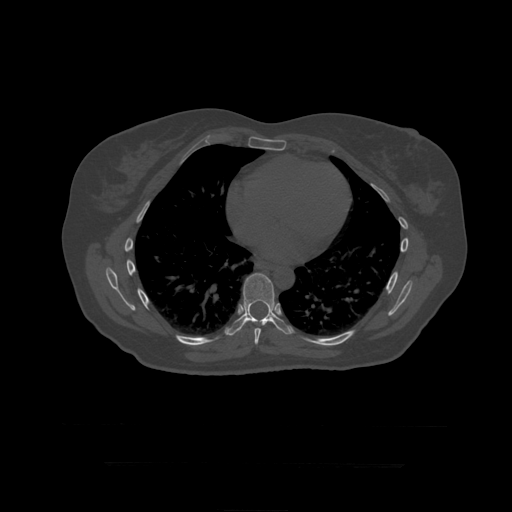
CT including the spine, one axial slice. Slice 268 of 399 in the series (ordered by position). Bone window (W 1800 / L 400 HU). 512 × 512 image matrix, field of view 450 × 450 mm. Patient age 41 years. Case-level facts recorded for this patient, not image findings: primary cancer: breast.
Annotated regions visible in this slice (semi-automatically segmented with operator editing):
- T8 vertebra: box from (x=254, y=328) to (x=262, y=345) px
- T9 vertebra: (x=226, y=273)–(x=291, y=336)